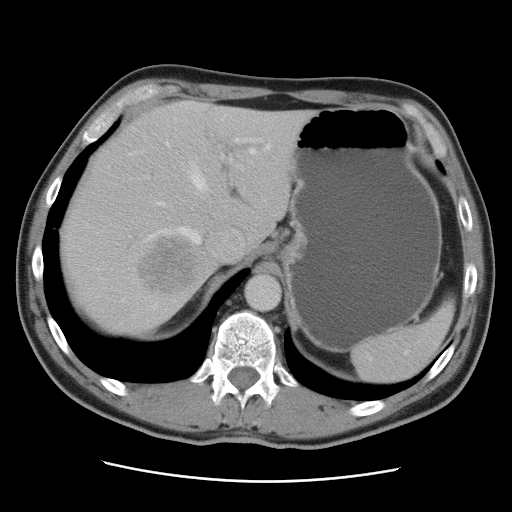
Contrast-enhanced abdominal CT, one axial slice. Position 68 of 89 along the scan axis. 120 kVp. Soft-tissue window (W 400 / L 40 HU). 5 mm slice thickness. 512 × 512 image matrix, field of view 366 × 366 mm. Male patient, age 59 years. Case-level facts recorded for this patient, not image findings: diagnosis: colorectal cancer liver metastases, imaged before liver resection; multiple liver metastases: yes; largest metastasis: 0.6 cm; chemotherapy before resection: no.
Annotated regions visible in this slice (expert manual segmentation):
- hepatic veins: bounding box [x1, y1, x2, y2] px = [97, 117, 270, 270]
- liver: [59, 101, 312, 337]
- planned liver remnant (the part of the liver to remain after resection): [106, 101, 312, 248]
- portal vein (with intrahepatic branches): [146, 138, 260, 179]
- liver metastasis: [141, 239, 197, 293]